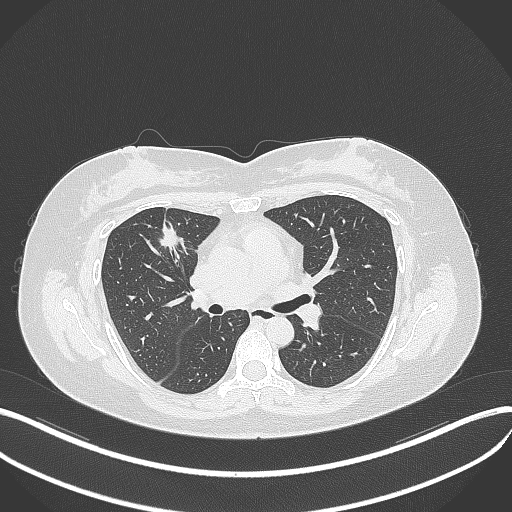
Chest CT, one axial slice. Slice 186 of 273 in the series (ordered by position). Lung window (W 1500 / L -600 HU). 1 mm slice thickness. 512 × 512 image matrix, field of view 400 × 400 mm. Patient: female, 42 years. From the clinical record (not read from this slice): clinical TNM (as recorded): T1b N0 M0.
Annotated regions visible in this slice (rectangle marked by the reading radiologist):
- lung tumour (recorded histology: adenocarcinoma): bounding box [x1, y1, x2, y2] px = [154, 218, 189, 257]